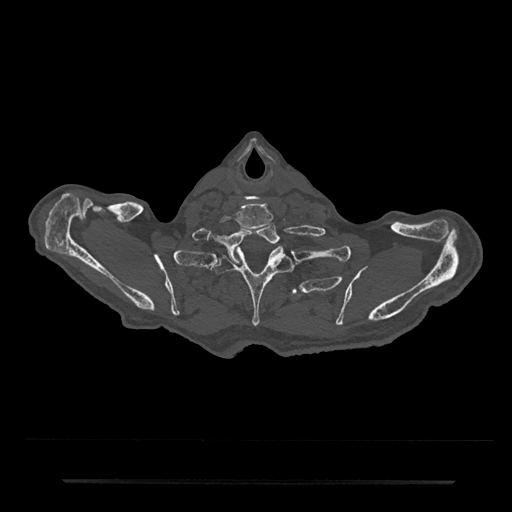
CT including the spine, one axial slice. Reconstruction kernel Br40s/3. 120 kVp. Bone window (W 1800 / L 400 HU). 0.5 mm slice thickness. 512 × 512 image matrix, field of view 427 × 427 mm. Male patient, age 74 years. Case-level facts recorded for this patient, not image findings: primary cancer: prostate.
Structures marked on this image (semi-automatically segmented with operator editing):
- T1 vertebra: bounding box <221,222,283,265> (left, top, right, bottom; pixels)
- T2 vertebra: <211,248,293,327>
- T3 vertebra: <290,287,299,298>